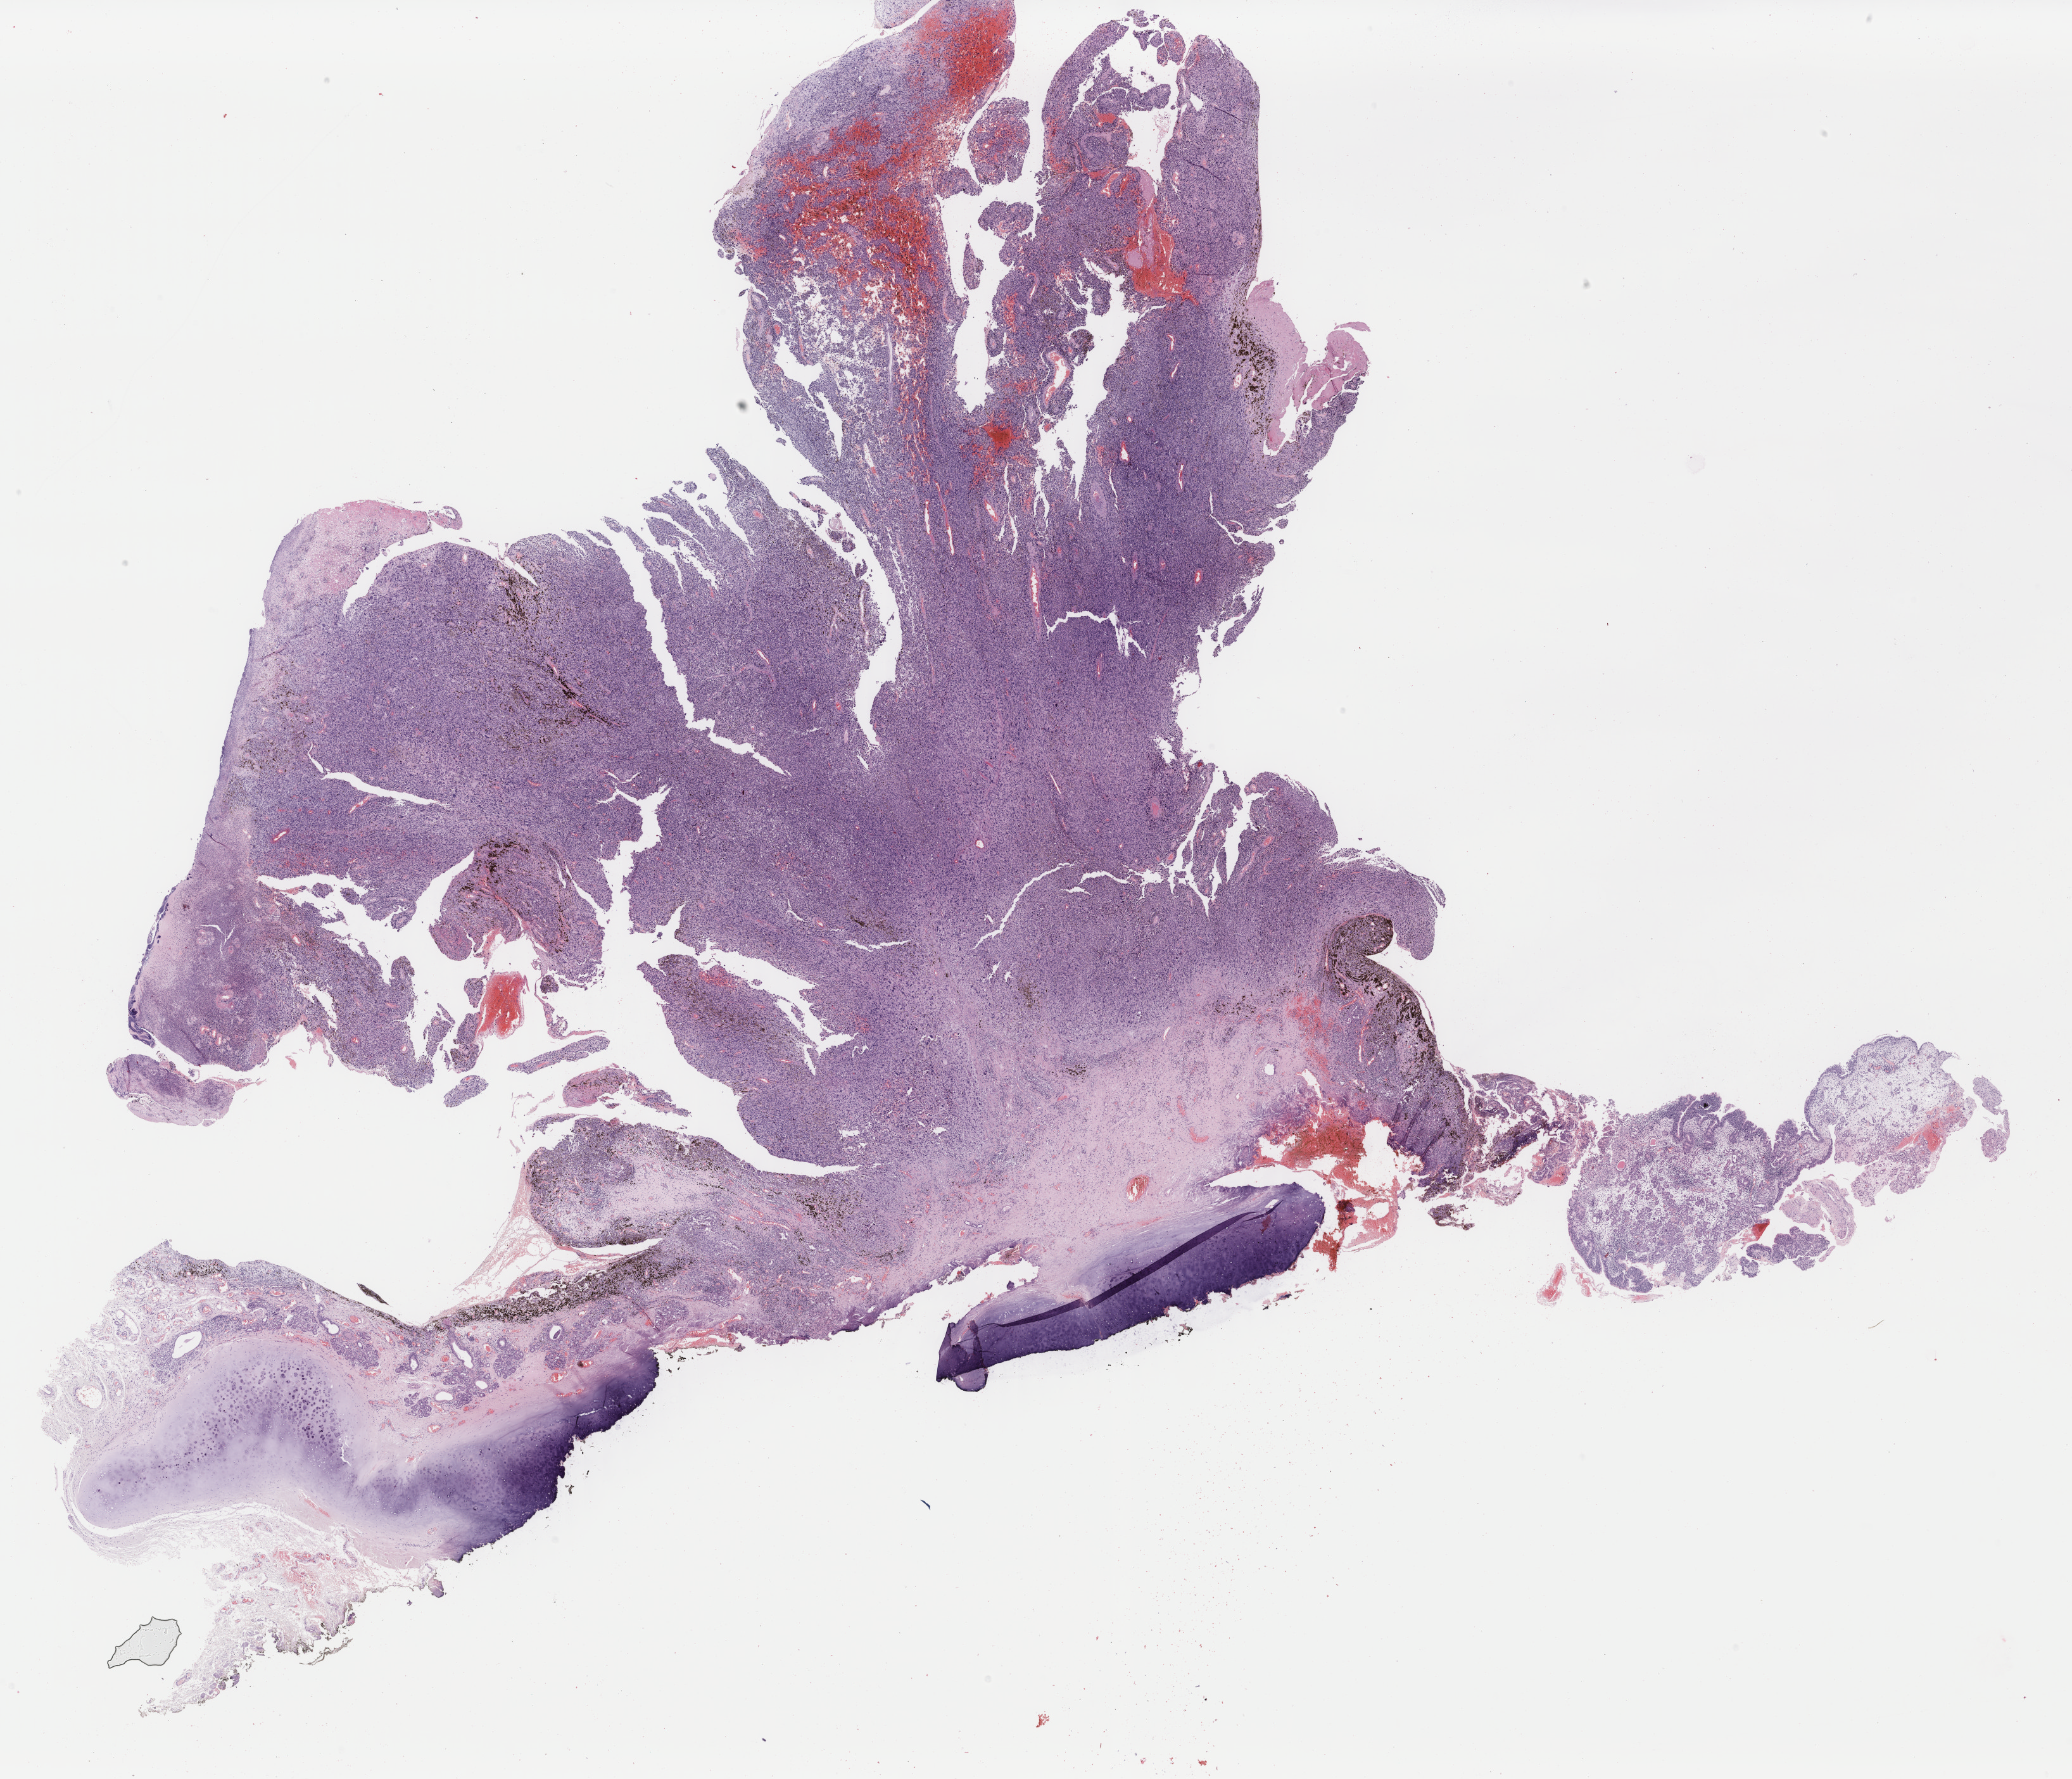
H&E whole-slide image, a low-resolution overview of the entire scanned area, about 26.0 x 22.3 mm; FFPE section; skin, primary tumour sample. Male patient; age at initial diagnosis 68 years.
• AJCC pathologic stage: IIB (7th edition)
• pathologic diagnosis: Malignant melanoma, NOS
• TNM: T4a N0 M0